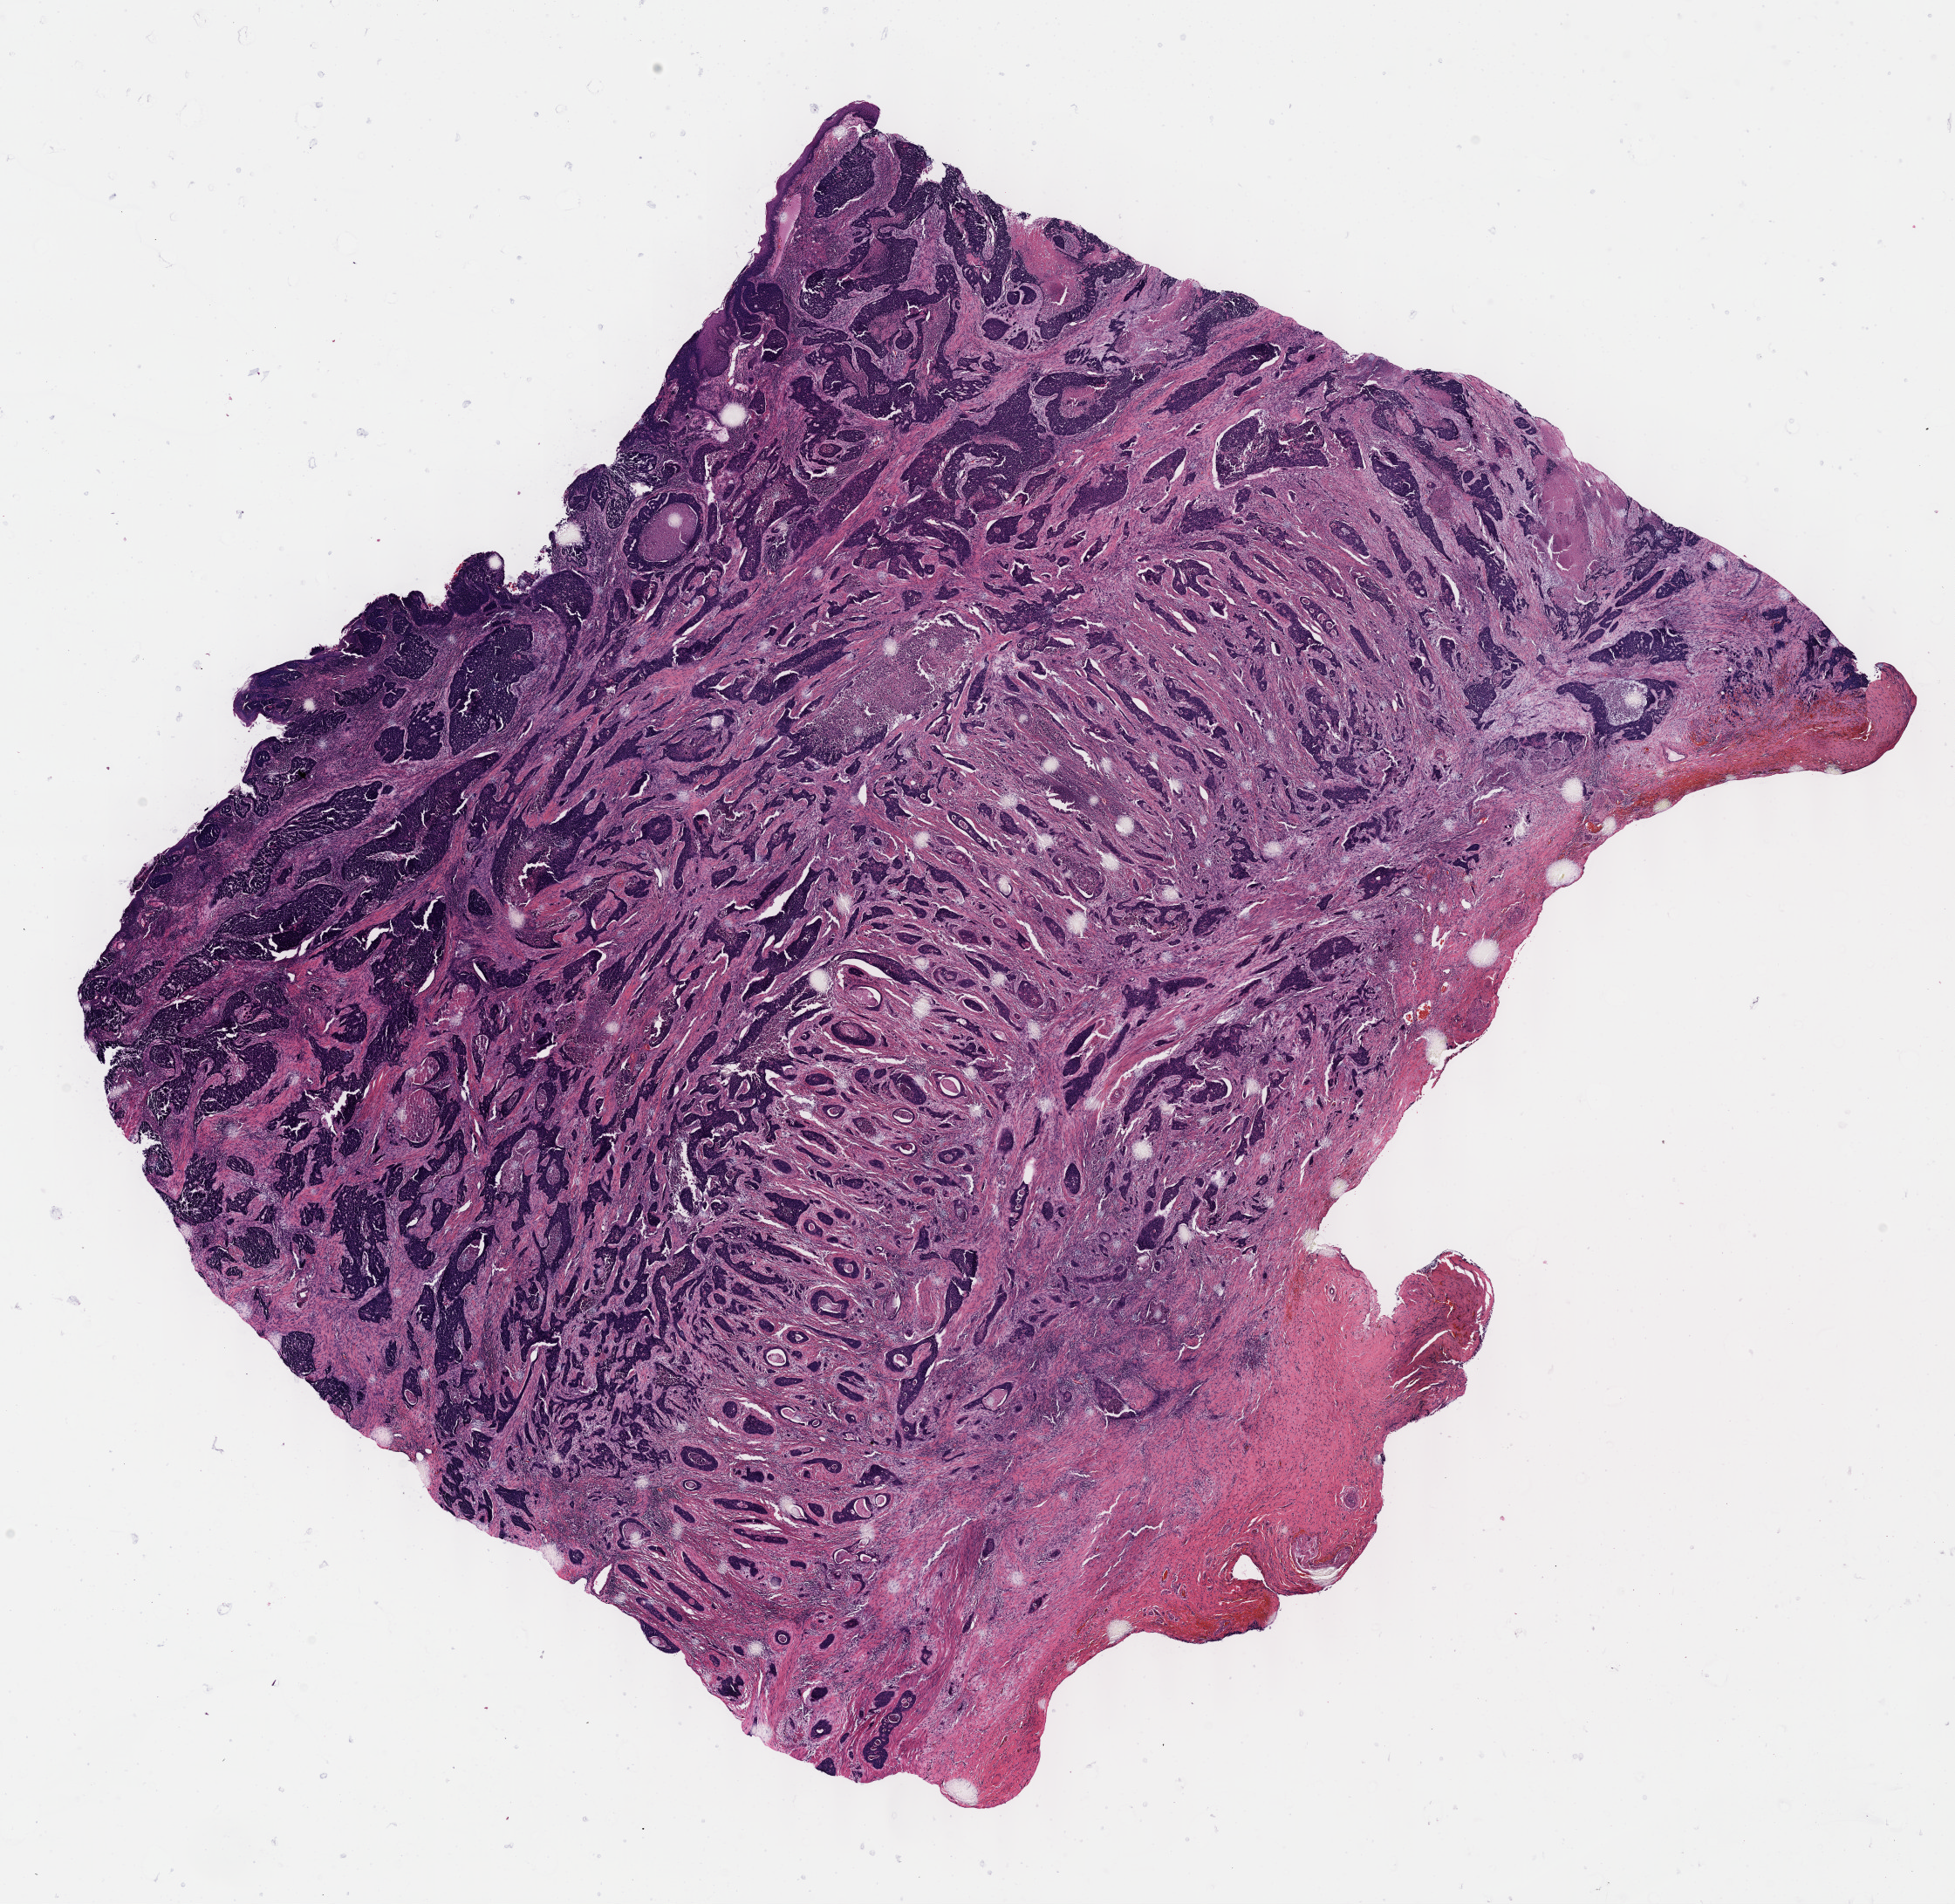
H&E whole-slide image — shown as a low-resolution overview of the whole scanned area (about 18.1 x 17.6 mm); FFPE section; esophagus, primary tumour sample. Male, age 57 years at initial diagnosis. Histologic grade: G3 (poorly differentiated).
Lymph nodes positive (case pathology): 1 of 9 examined. AJCC pathologic stage: IIIA. Pathologic diagnosis: Squamous cell carcinoma, NOS (upper third of esophagus). TNM: T3 N1 M0.